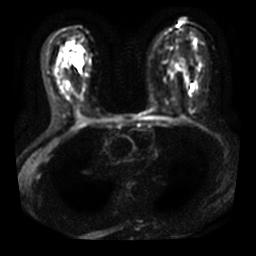
Breast MRI, one axial slice; slice 19 of 40 in the series (ordered by position); diffusion-weighted series; image 2 of 4 stored at this slice position (different b-values; order by instance number); 3 T; 5 mm slice thickness; 256 × 256 image matrix. Female patient.
Annotated regions visible in this slice (expert manual segmentation):
- tumour on diffusion-weighted imaging: bounding box (x1, y1, x2, y2) in pixels: (72, 53, 82, 69)